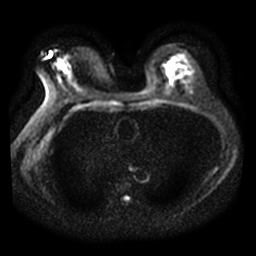
Breast MRI, one axial slice. Slice 23 of 40 in the series (ordered by position). Diffusion-weighted series; image 2 of 4 stored at this slice position (different b-values; order by instance number). 3 T. 256 × 256 image matrix. Female patient.
Outlined on this slice (outlined manually by an expert reader):
- tumour on diffusion-weighted imaging: bounding box (x1, y1, x2, y2) in pixels: (58, 57, 60, 59)